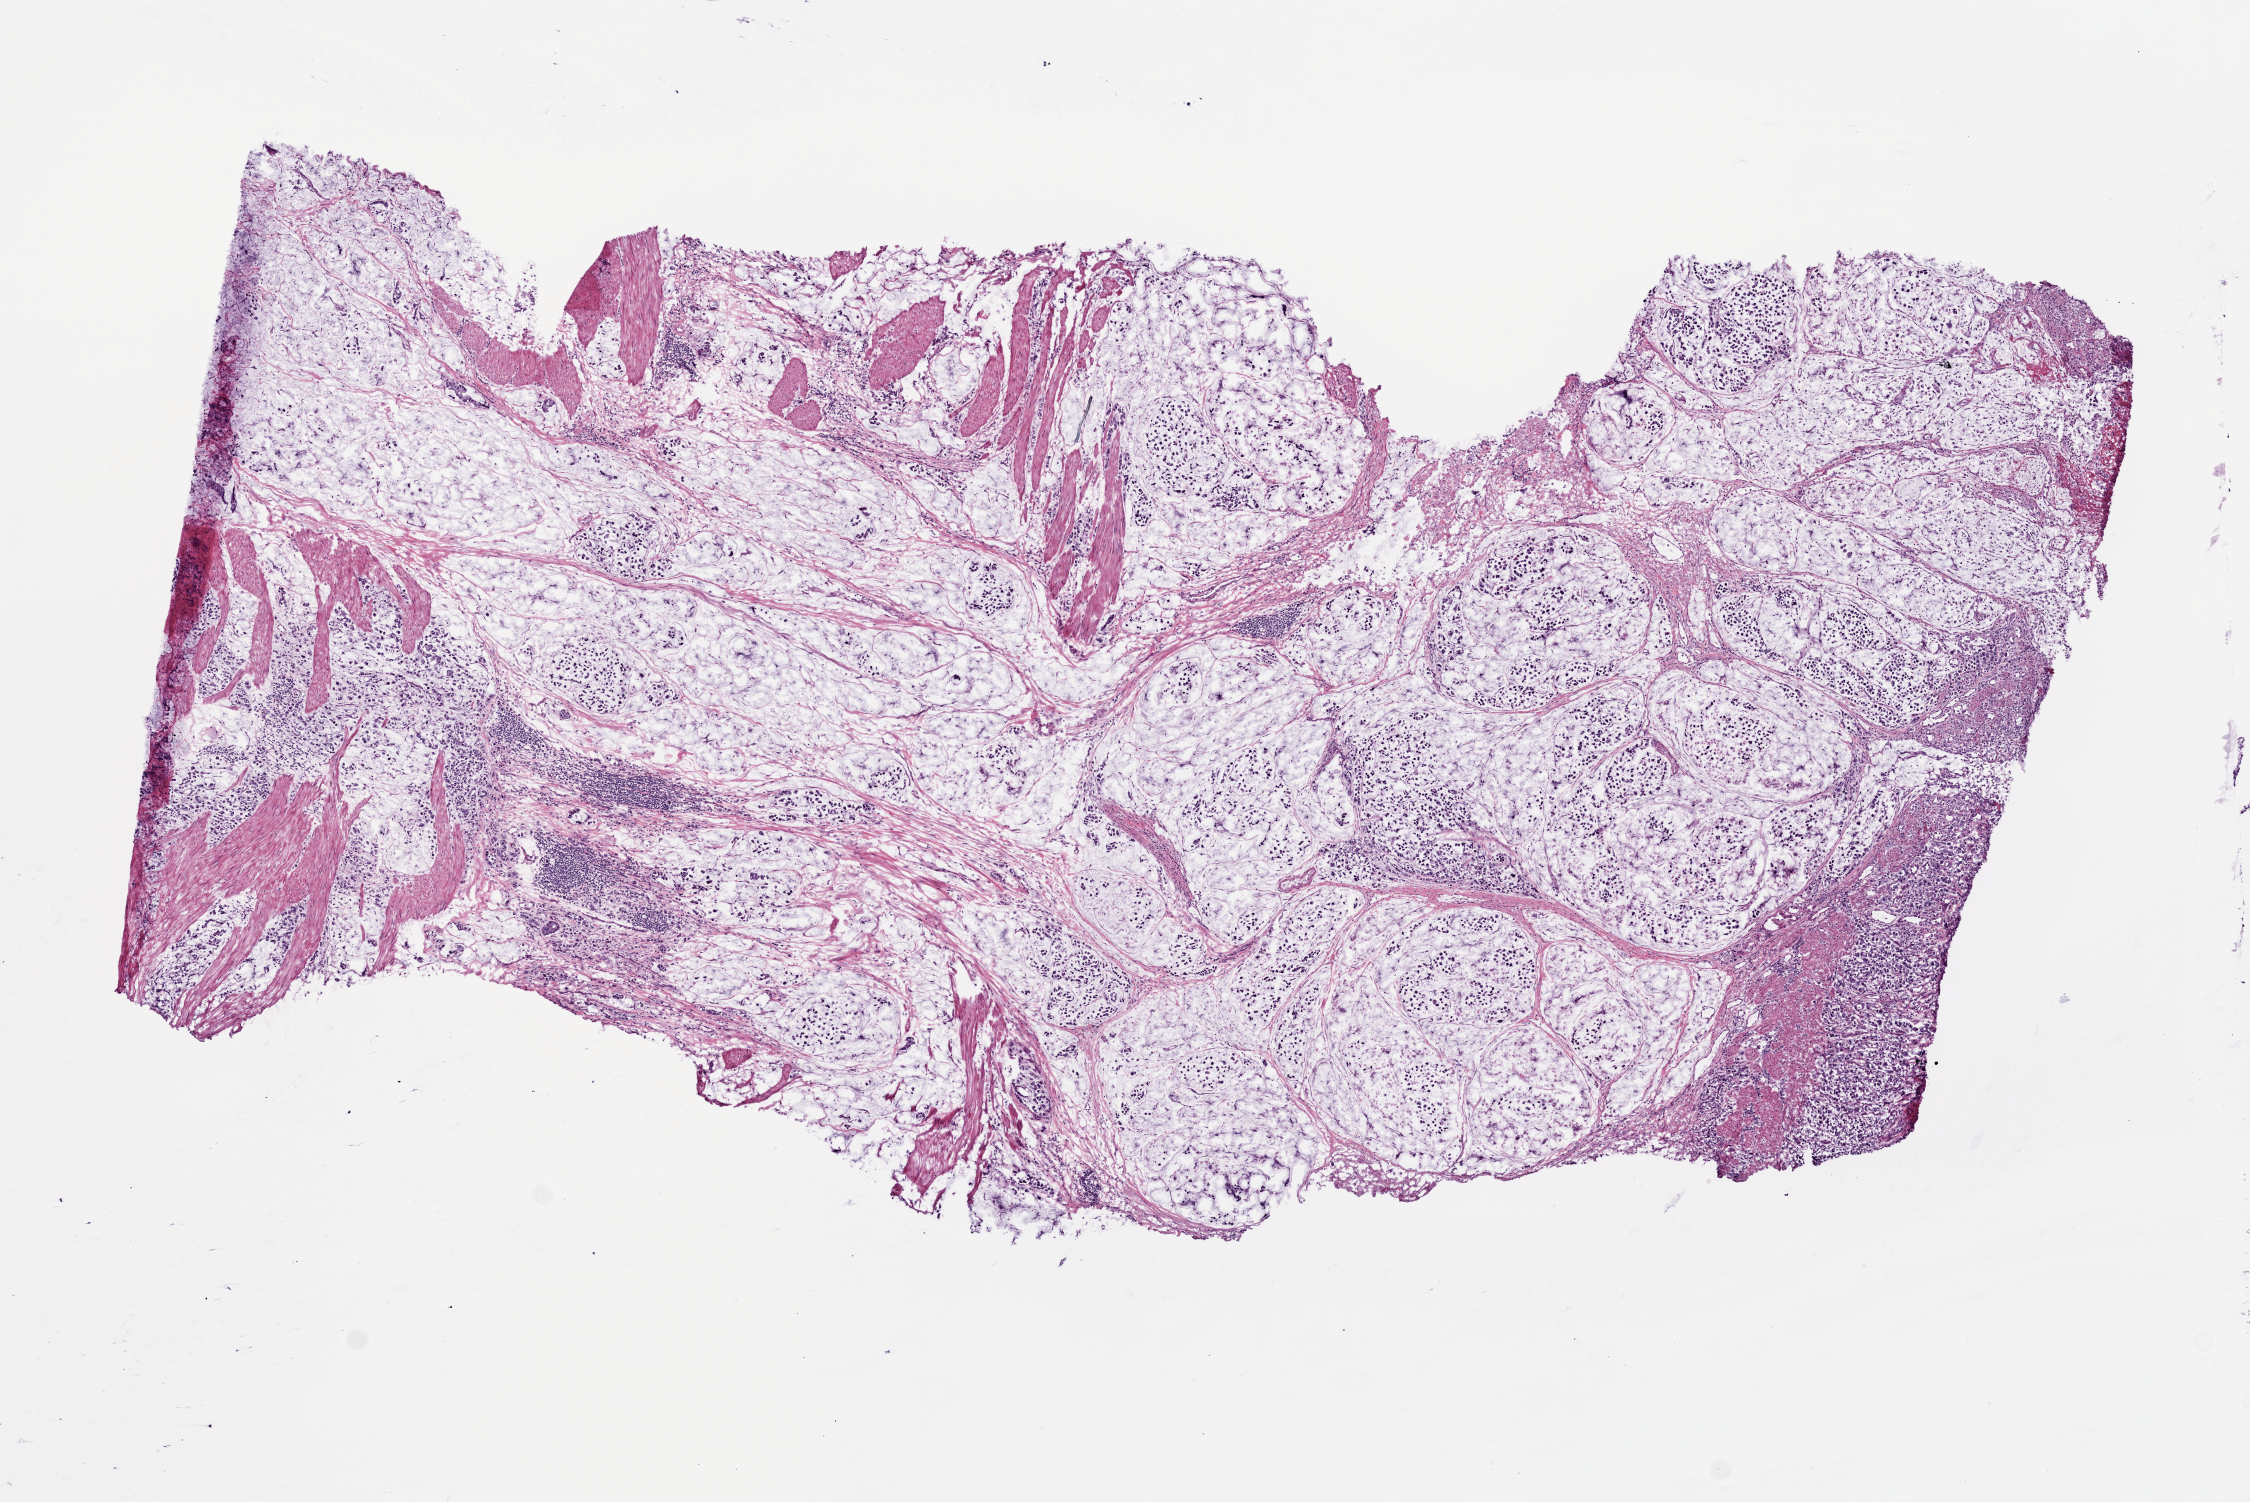
Whole-slide histology image, H&E-stained — shown as a low-resolution overview of the whole scanned area (about 9.0 x 6.0 mm), frozen section from the bottom of the tissue portion, sample: primary tumour, stomach. Male patient; age at initial diagnosis 74 years. Histologic grade: G3 (poorly differentiated). Pathologist review of this section (percent, as recorded): tumour cells 85%, tumour nuclei 80%, normal cells 0%, stromal cells 15%, necrosis 0%.
- lymph nodes positive (case pathology): 11 of 12 examined
- AJCC pathologic stage: IIIA (7th edition)
- TNM: T3 N2 M0
- diagnosis: Mucinous adenocarcinoma (body of stomach)